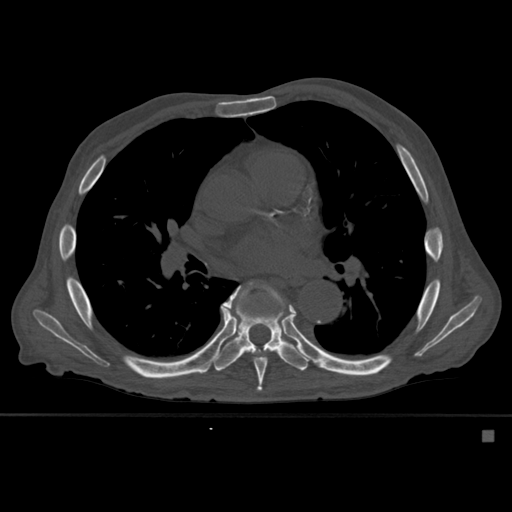
CT including the spine, one axial slice; slice 358 of 527 in the series (ordered by position); bone window (W 1800 / L 400 HU); 1.5 mm slice thickness; 512 × 512 image matrix, field of view 373 × 373 mm. Male patient, age 78 years. From the clinical record (not read from this slice): primary cancer: prostate.
Annotated regions visible in this slice (semi-automatically segmented with operator editing):
- T7 vertebra: bounding box <224,281,296,392> (left, top, right, bottom; pixels)
- T8 vertebra: <212,283,308,371>